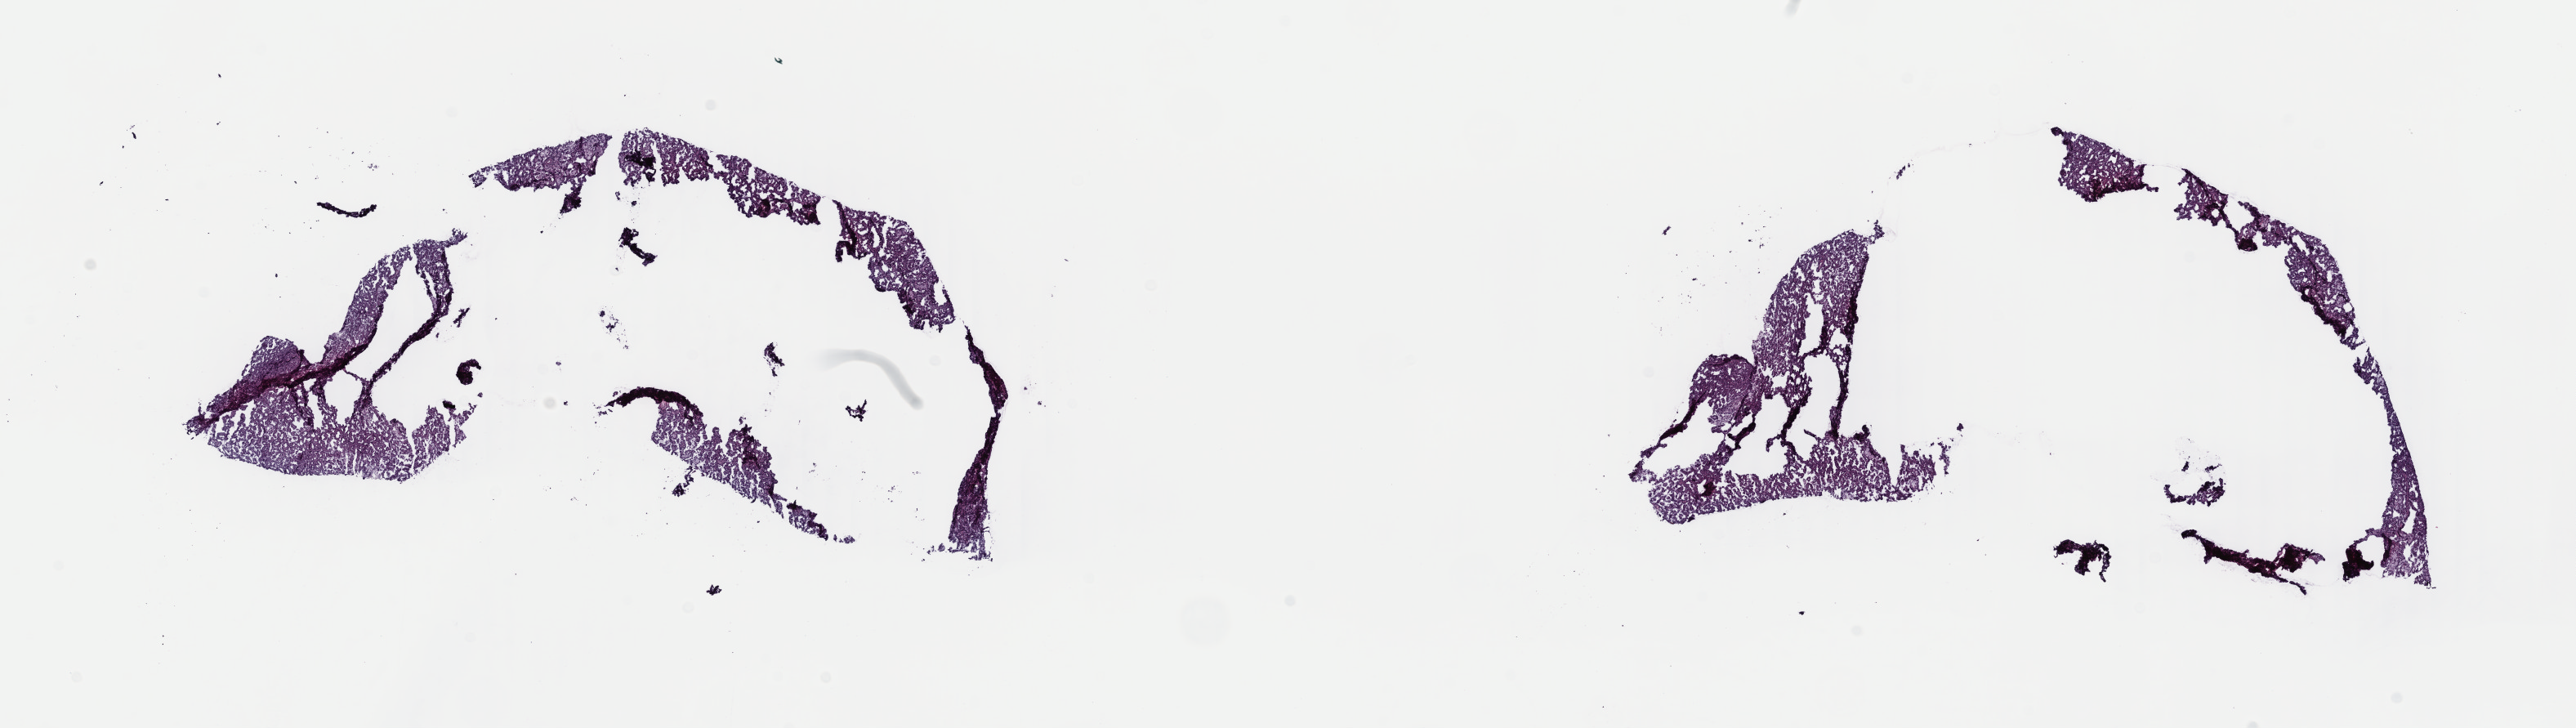
Digitized H&E tissue section (whole slide), whole scanned area (about 24.9 x 7.0 mm) shown as a low-resolution overview; frozen section from the top of the tissue portion; primary tumour sample from the kidney. Male patient; age at initial diagnosis 66 years. Slide review estimates, as recorded: tumour cells 75%, tumour nuclei 80%, normal cells 0%, stromal cells 25%, necrosis 0%. Infiltration values recorded for this section: lymphocyte infiltration 0%, monocyte infiltration 100%, neutrophil infiltration 0%.
Pathologic diagnosis: Papillary adenocarcinoma, NOS. Laterality: left. AJCC pathologic stage: I (7th edition).